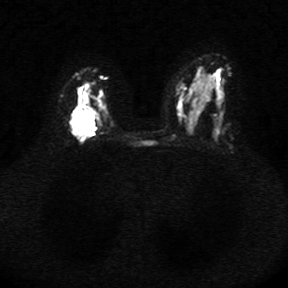
Breast MRI, one axial slice. Slice 18 of 34 in the series (ordered by position). Diffusion-weighted series; image 2 of 4 stored at this slice position (different b-values; order by instance number). 1.5 T. 5 mm slice thickness. 288 × 288 image matrix, field of view 340 × 340 mm. Female patient.
Outlined on this slice (outlined manually by an expert reader):
- tumour on diffusion-weighted imaging: bounding box [x1, y1, x2, y2] px = [69, 108, 94, 136]